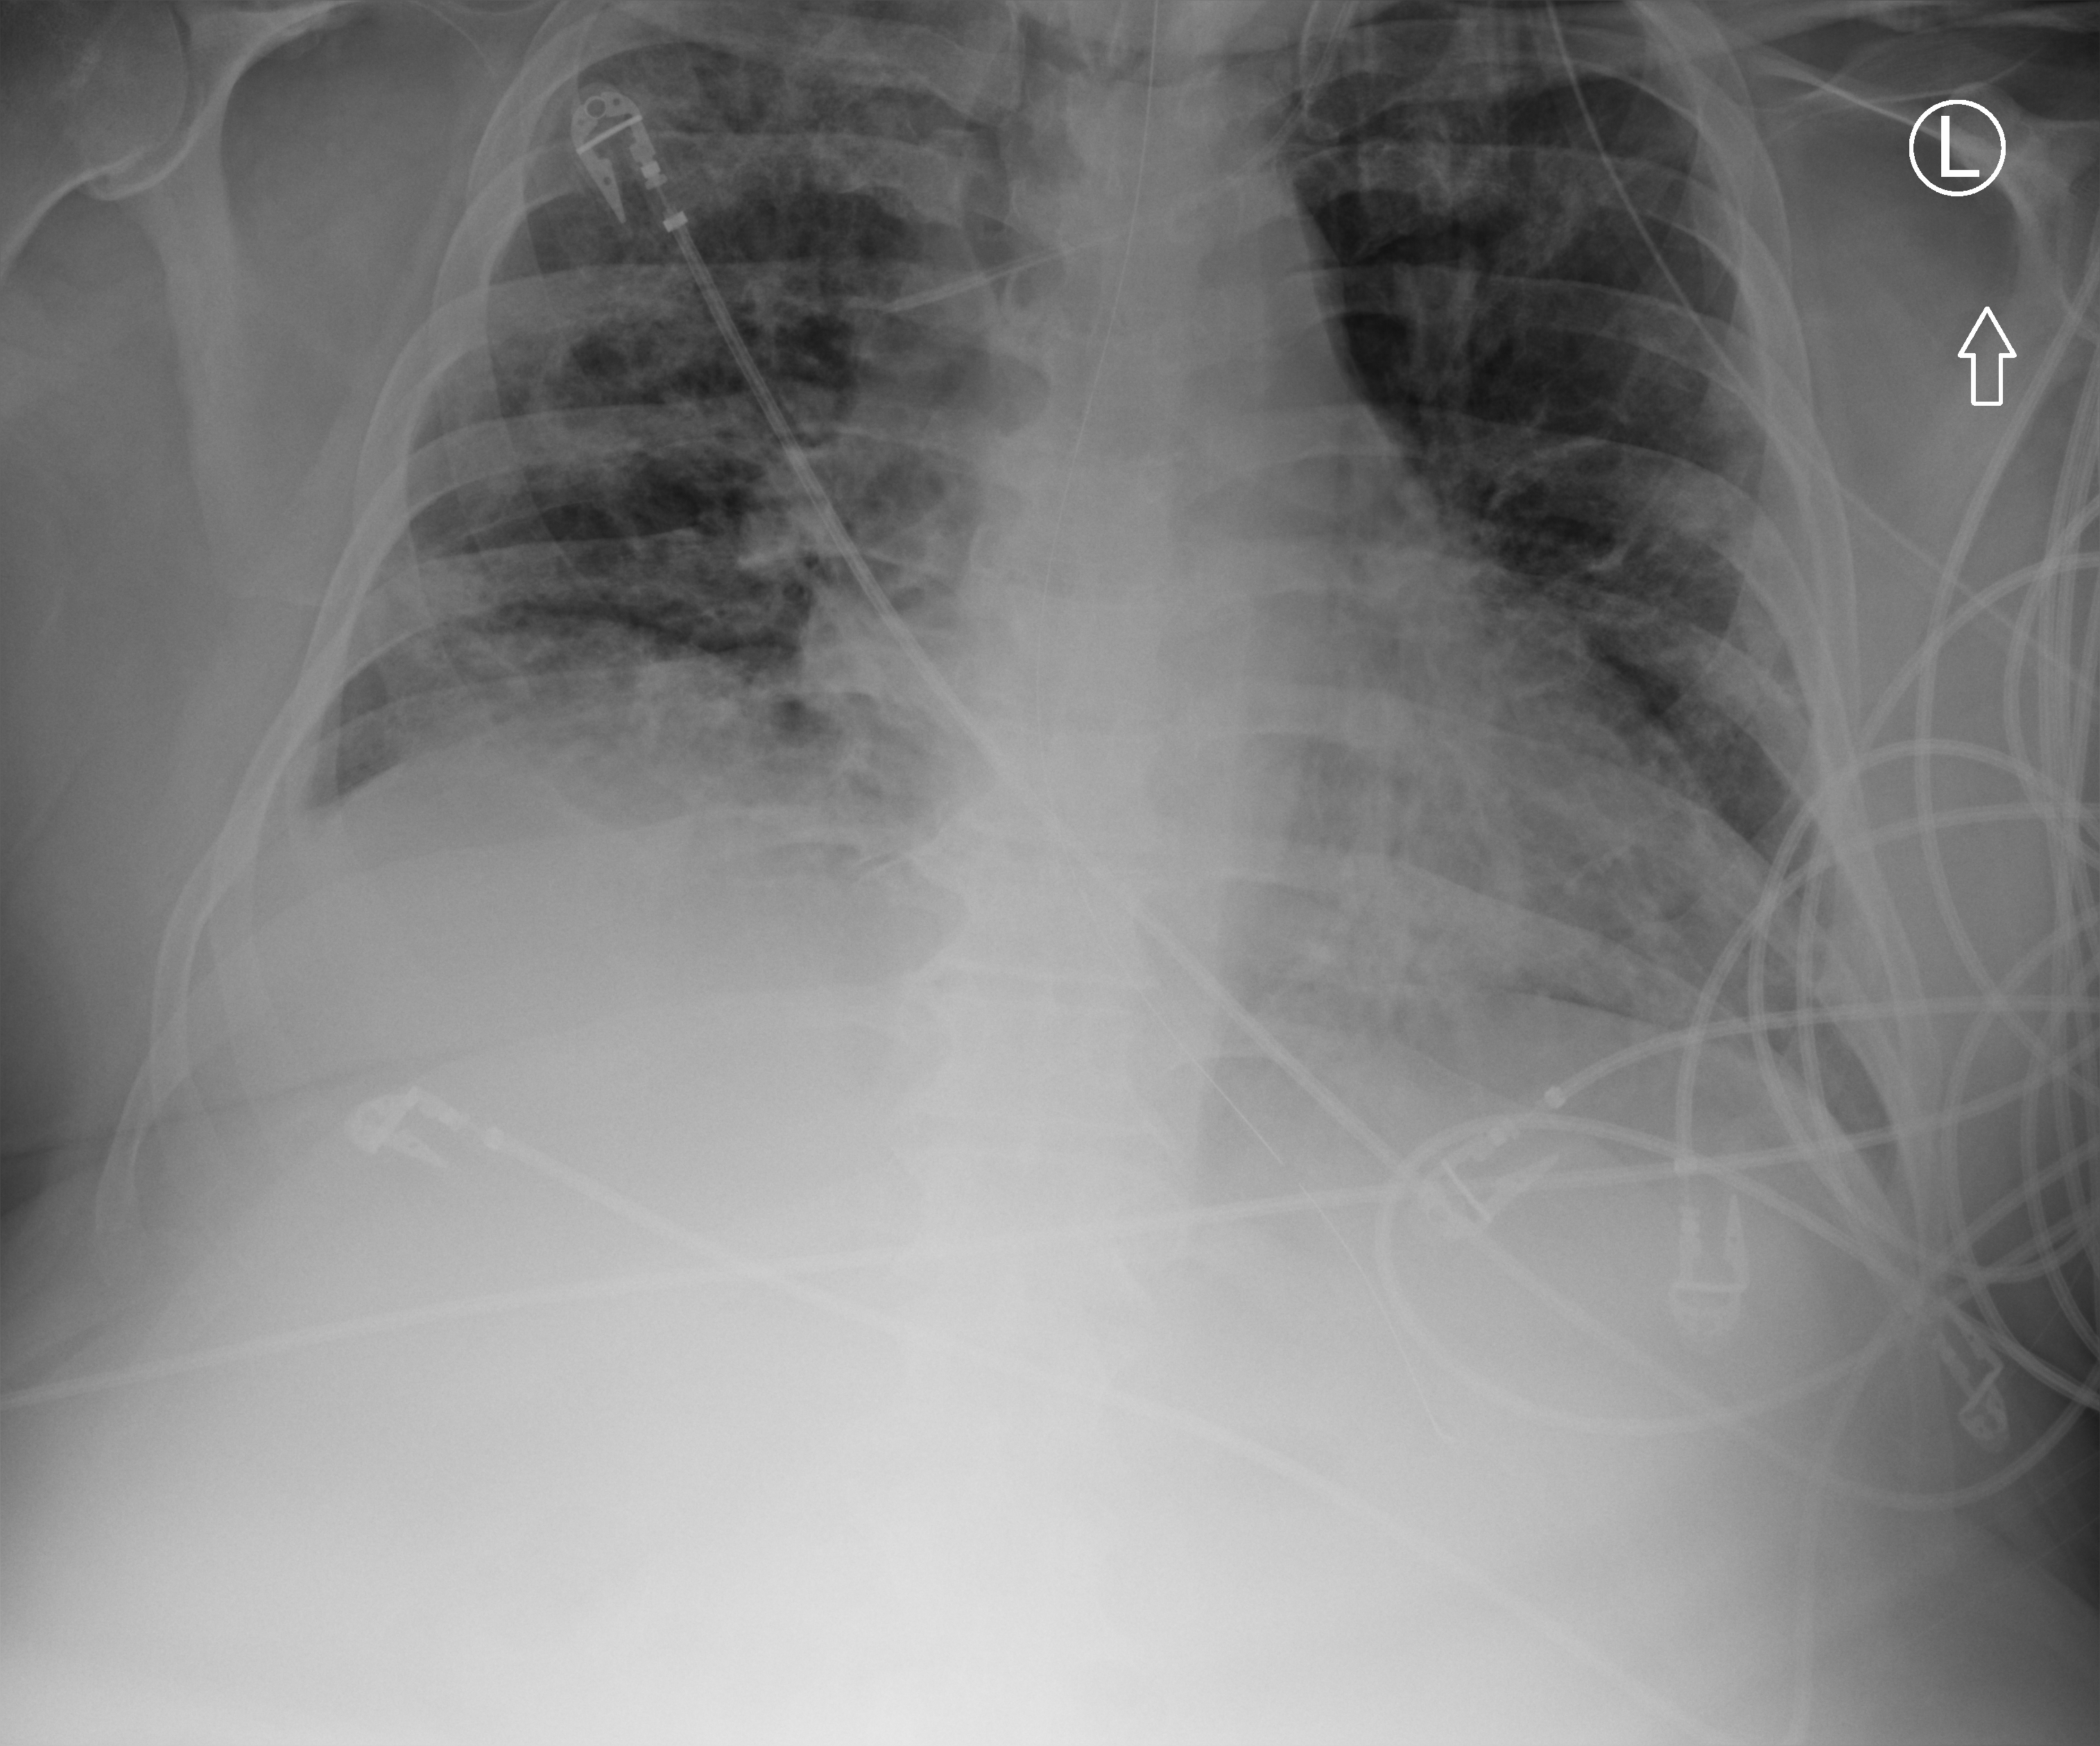
Bedside chest radiograph (computed radiography); anteroposterior (AP) projection. Male patient hospitalised with COVID-19, age 18–59 years.
From the hospital-stay record, not from the radiograph (when in the stay this image was taken is not recorded): chronic kidney disease (admission record): no.